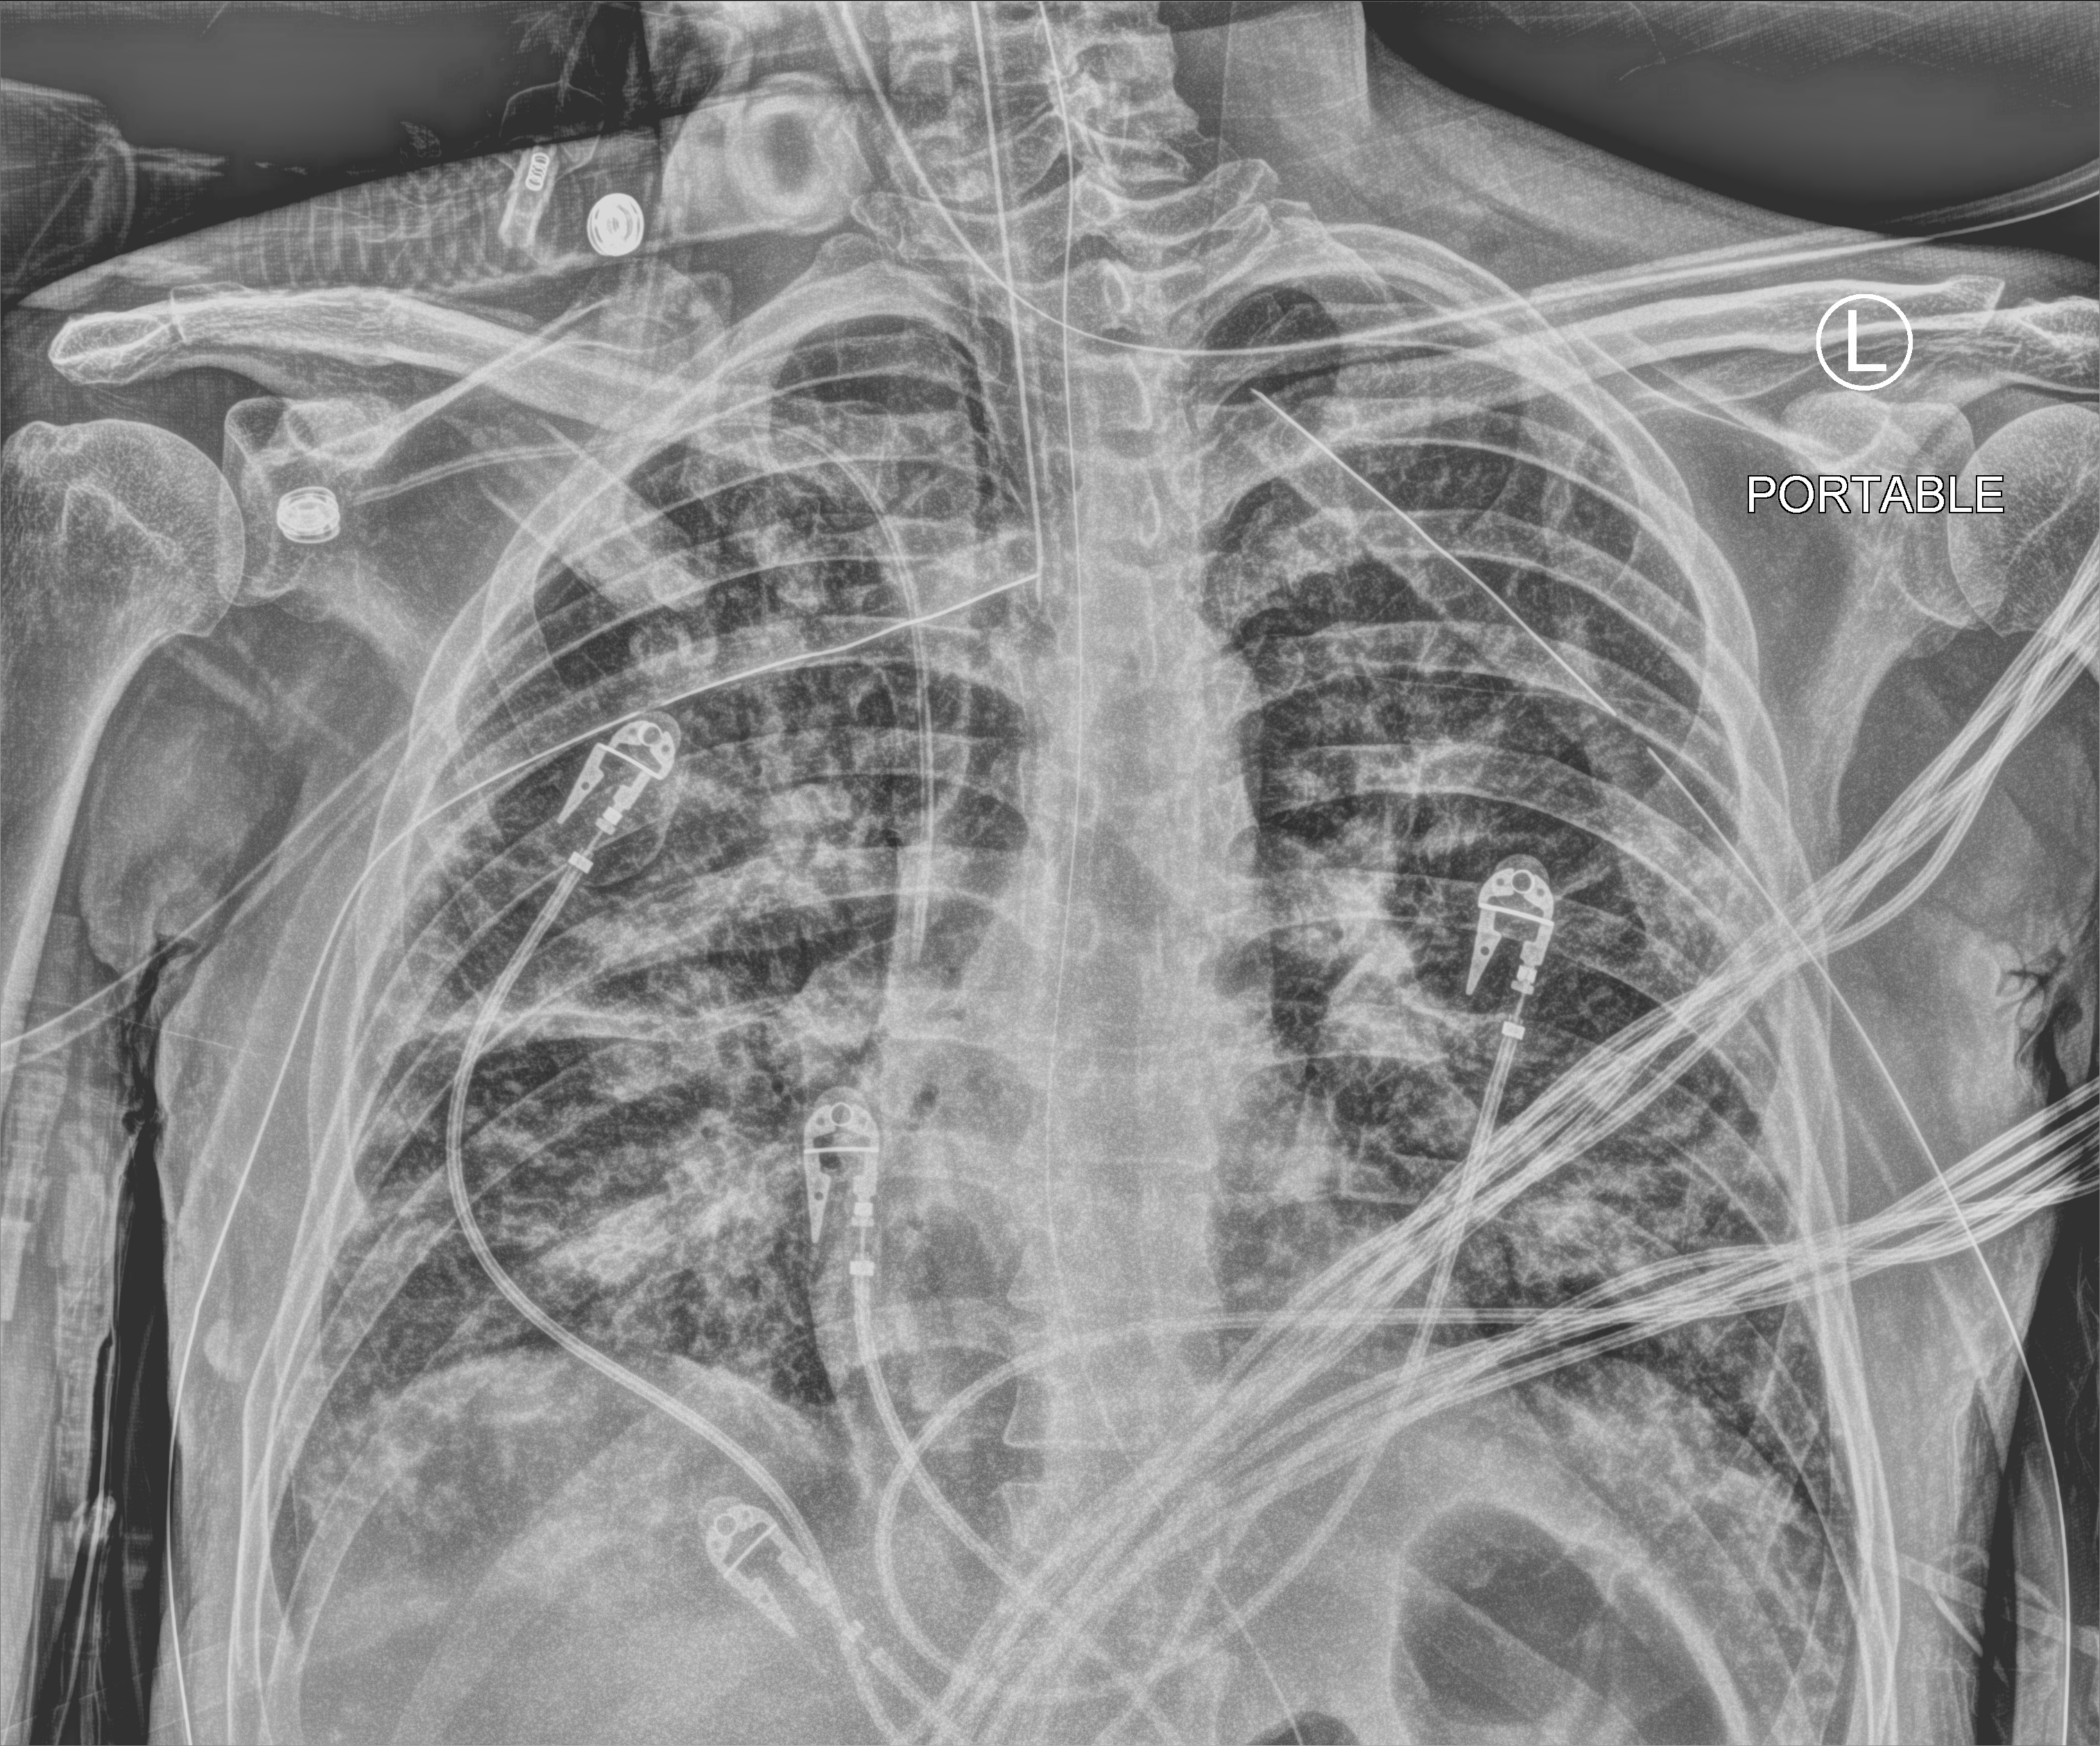
Portable chest radiograph. Male patient hospitalised with COVID-19, age 18–59 years.
Admission-level facts for this patient (not findings on this image; timing relative to this image not recorded):
- mechanically ventilated during this hospital stay: yes
- admitted to intensive care during this hospital stay: yes
- diabetes (admission record): yes